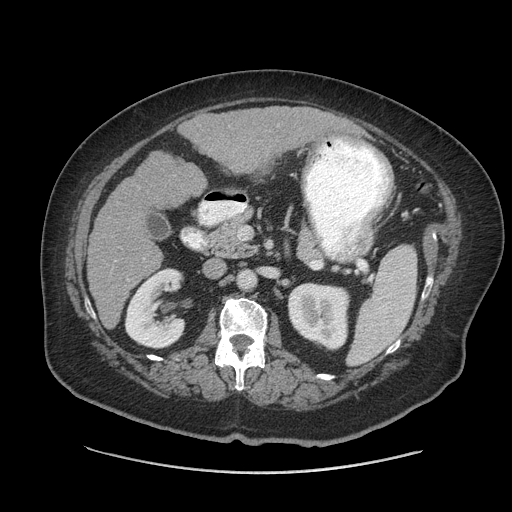
Contrast-enhanced abdominal CT (liver protocol), one axial slice. Position 29 of 91 along the scan axis. 140 kVp. Soft-tissue window (W 400 / L 40 HU). 512 × 512 image matrix, field of view 420 × 420 mm. From the clinical record (not read from this slice): diagnosis: hepatocellular carcinoma (patient treated with transarterial chemoembolisation; whether this scan precedes or follows treatment is not stated here); TNM stage (as recorded): Stage-I; Child-Pugh class: A; tumour differentiation: well differentiated; tumour nodularity: uninodular.
Annotated regions visible in this slice (semi-automatically segmented with operator editing):
- liver parenchyma outside the tumour (the mass and vessels are separate outlines, so this box may not span the whole liver): box from (x=88, y=106) to (x=350, y=328) px